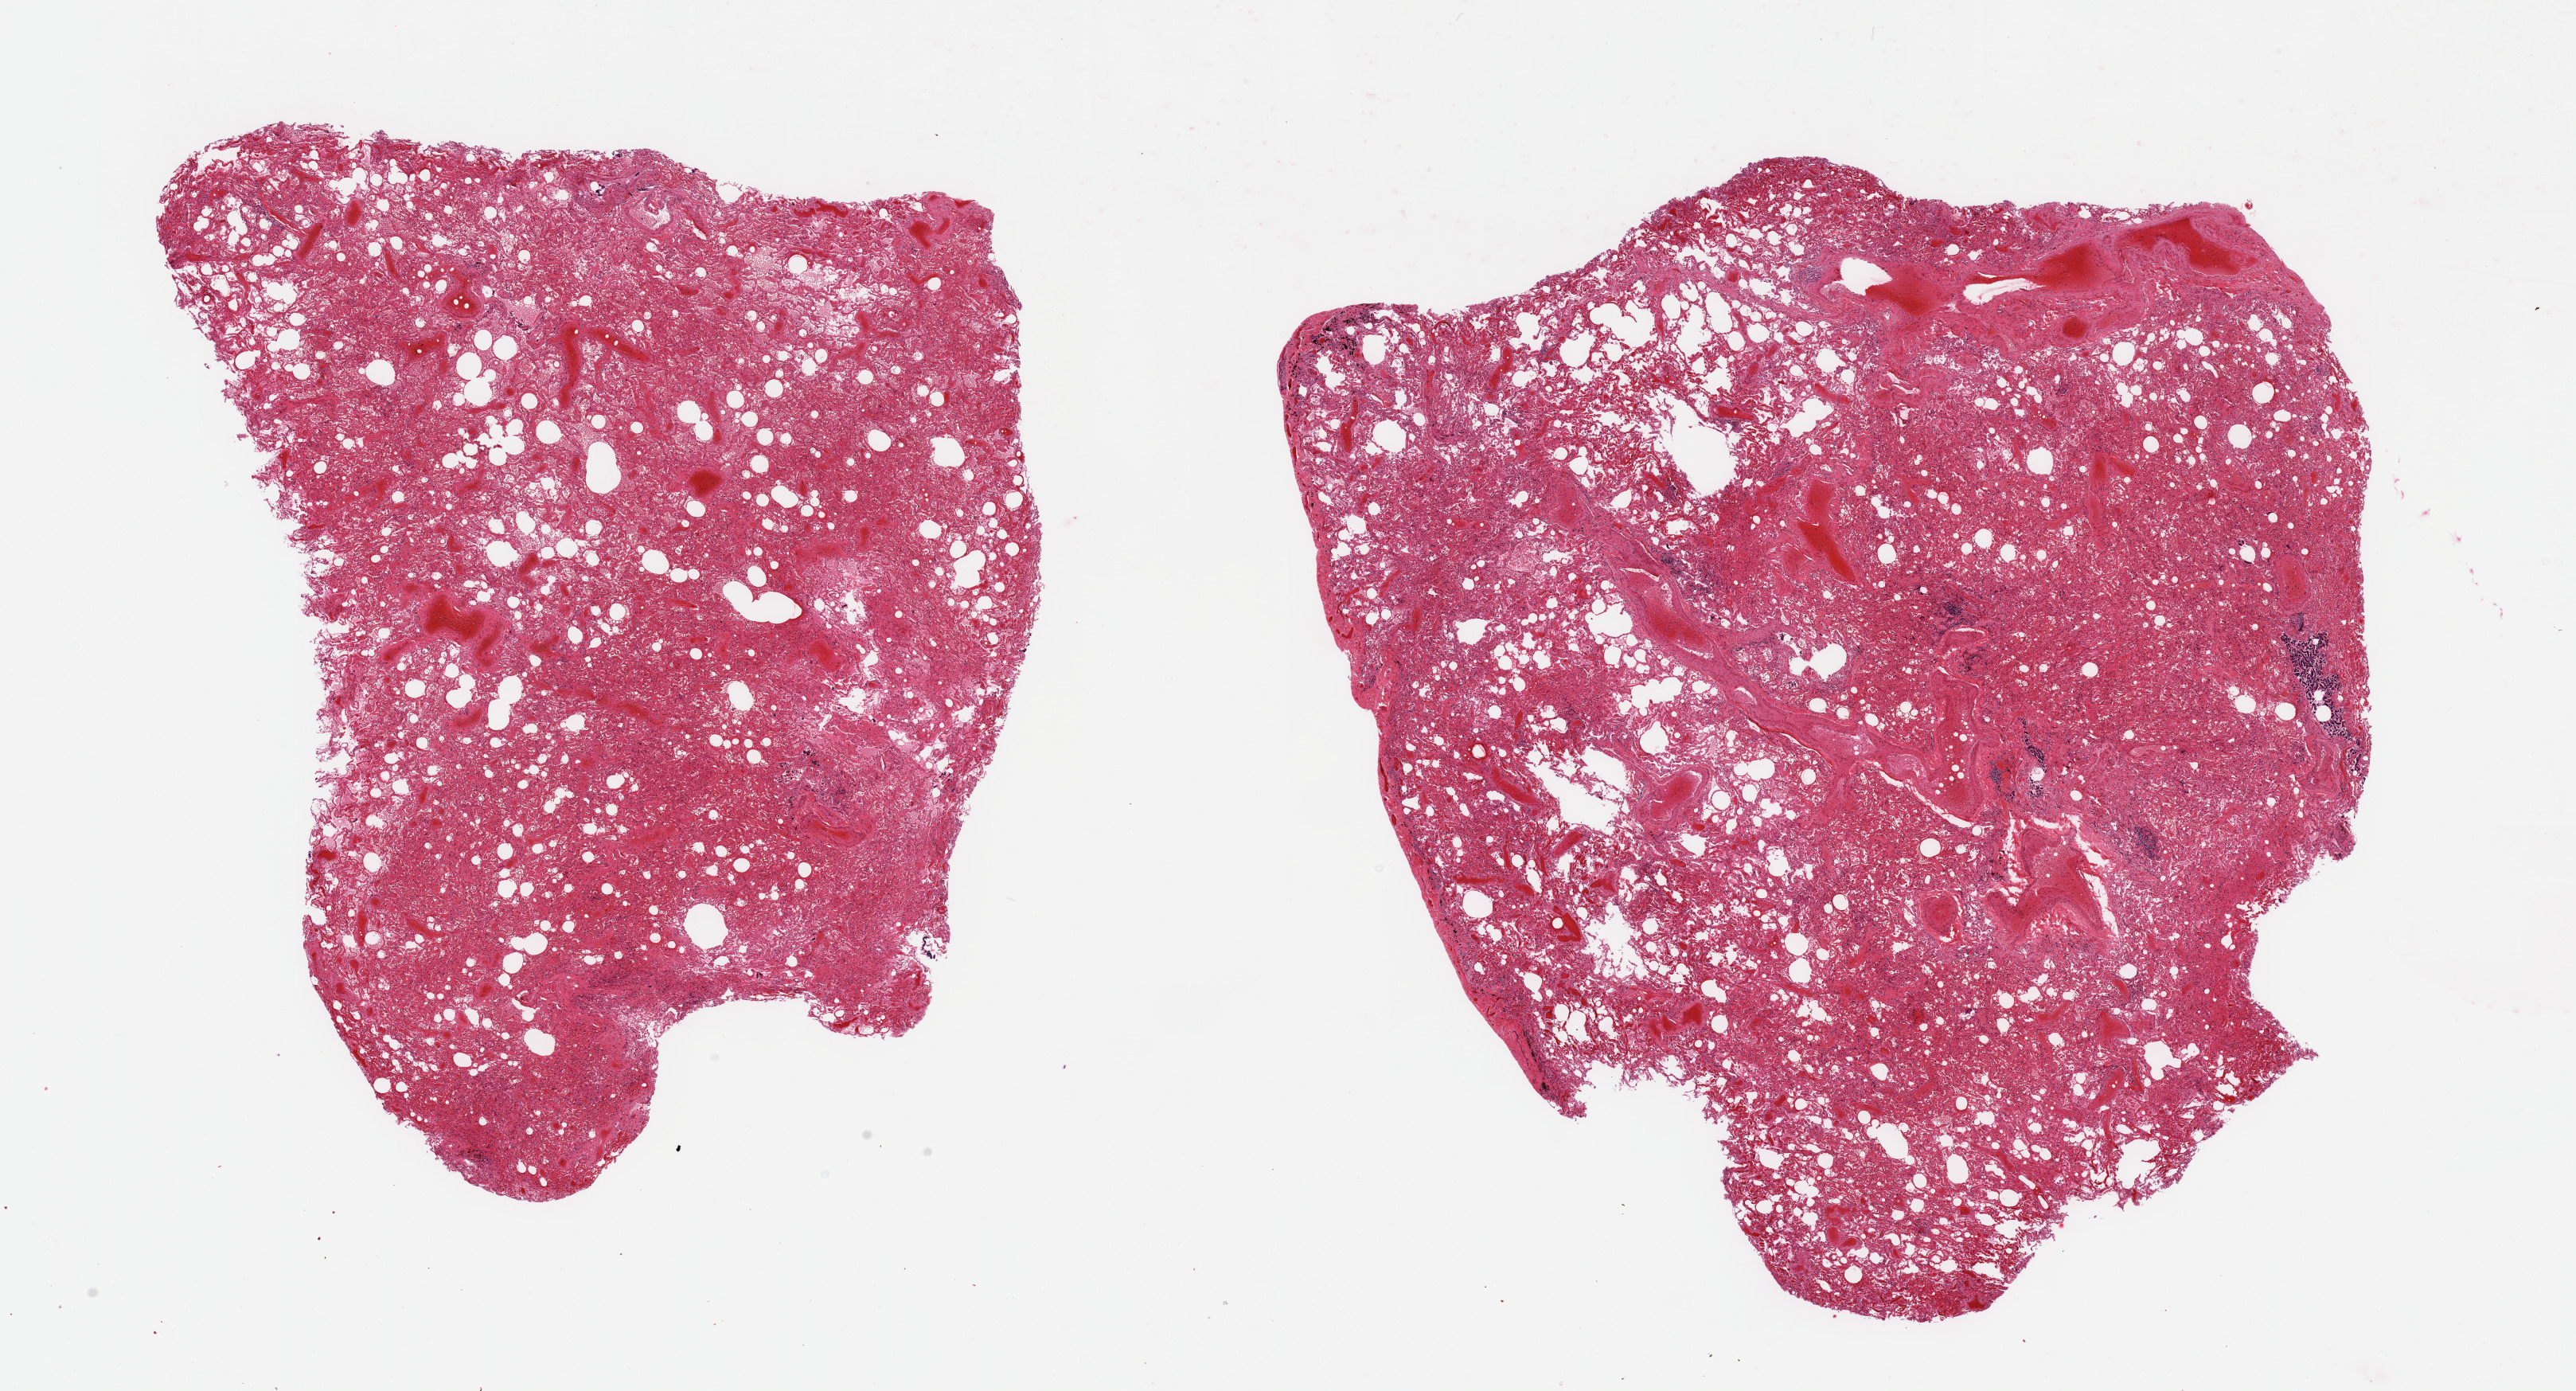
Digitized H&E-stained section, shown as a low-resolution overview of the whole scanned area (about 25.6 x 13.8 mm, acquisition: 20x scan); PAXgene-fixed paraffin-embedded (PFPE) section; sampled site (target tissue): lung; tissue donor sample. Male donor.
- pathologist's review note for this sample: 2 pieces, moderate congestion/atalectasis